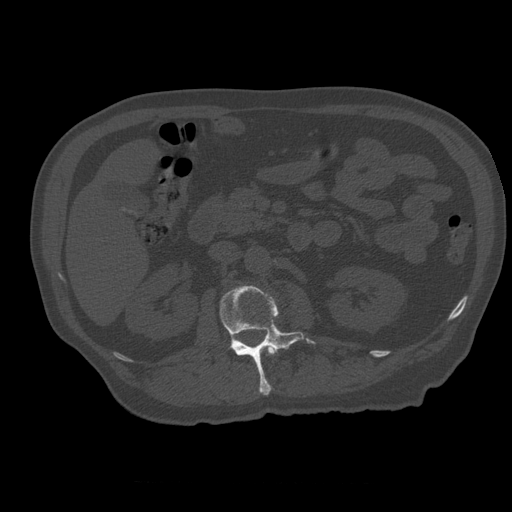
CT including the spine, one axial slice. Slice 215 of 399 in the series (ordered by position). Reconstruction kernel STANDARD. Bone window (W 1800 / L 400 HU). 512 × 512 image matrix, field of view 407 × 407 mm. Patient age 73 years. Case-level facts recorded for this patient, not image findings: primary cancer: prostate; vertebrae with lytic lesions (as recorded): L2.
Annotated regions visible in this slice (semi-automatic segmentation, software-assisted and operator-edited):
- L1 vertebra: bounding box (x1, y1, x2, y2) in pixels: (267, 346, 279, 355)
- L2 vertebra: (220, 286, 305, 396)